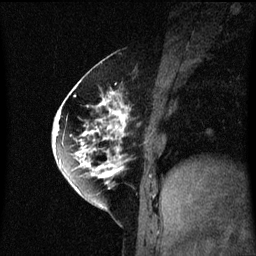
Breast MRI (dynamic contrast-enhanced), one sagittal slice. Slice 23 of 60 in the series (ordered by position). Dynamic contrast-enhanced series, image 2 of 3 at this slice position (ordered by acquisition). 1.5 T. TE 4.2 ms, TR 8.4 ms. 2 mm slice thickness. 256 × 256 image matrix, field of view 200 × 200 mm. Female patient, age 60 years.
Outlined on this slice (semi-automatic segmentation, software-assisted and operator-edited):
- analysis volume of interest (the breast-tissue region the enhancement analysis was run in; not a lesion): bounding box [x1, y1, x2, y2] px = [64, 70, 133, 195]
- tumour enhancement mask (voxels above the 70 % enhancement threshold inside the analysis volume of interest): [64, 70, 131, 191]